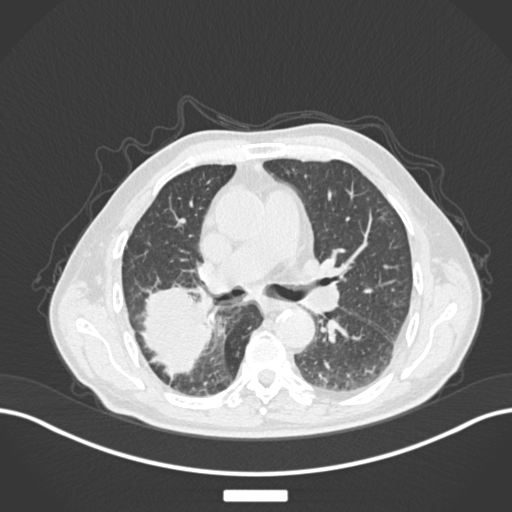
Chest CT, one axial slice; slice 100 of 201 in the series (ordered by position); 120 kVp; lung window (W 1500 / L -600 HU); 1 mm slice thickness; 512 × 512 image matrix. Male patient, age 72 years. From the clinical record (not read from this slice): clinical TNM (as recorded): T3 N2 M0.
Structures marked on this image (rectangle marked by the reading radiologist):
- lung tumour (recorded histology: adenocarcinoma): box from (x=137, y=284) to (x=217, y=377) px